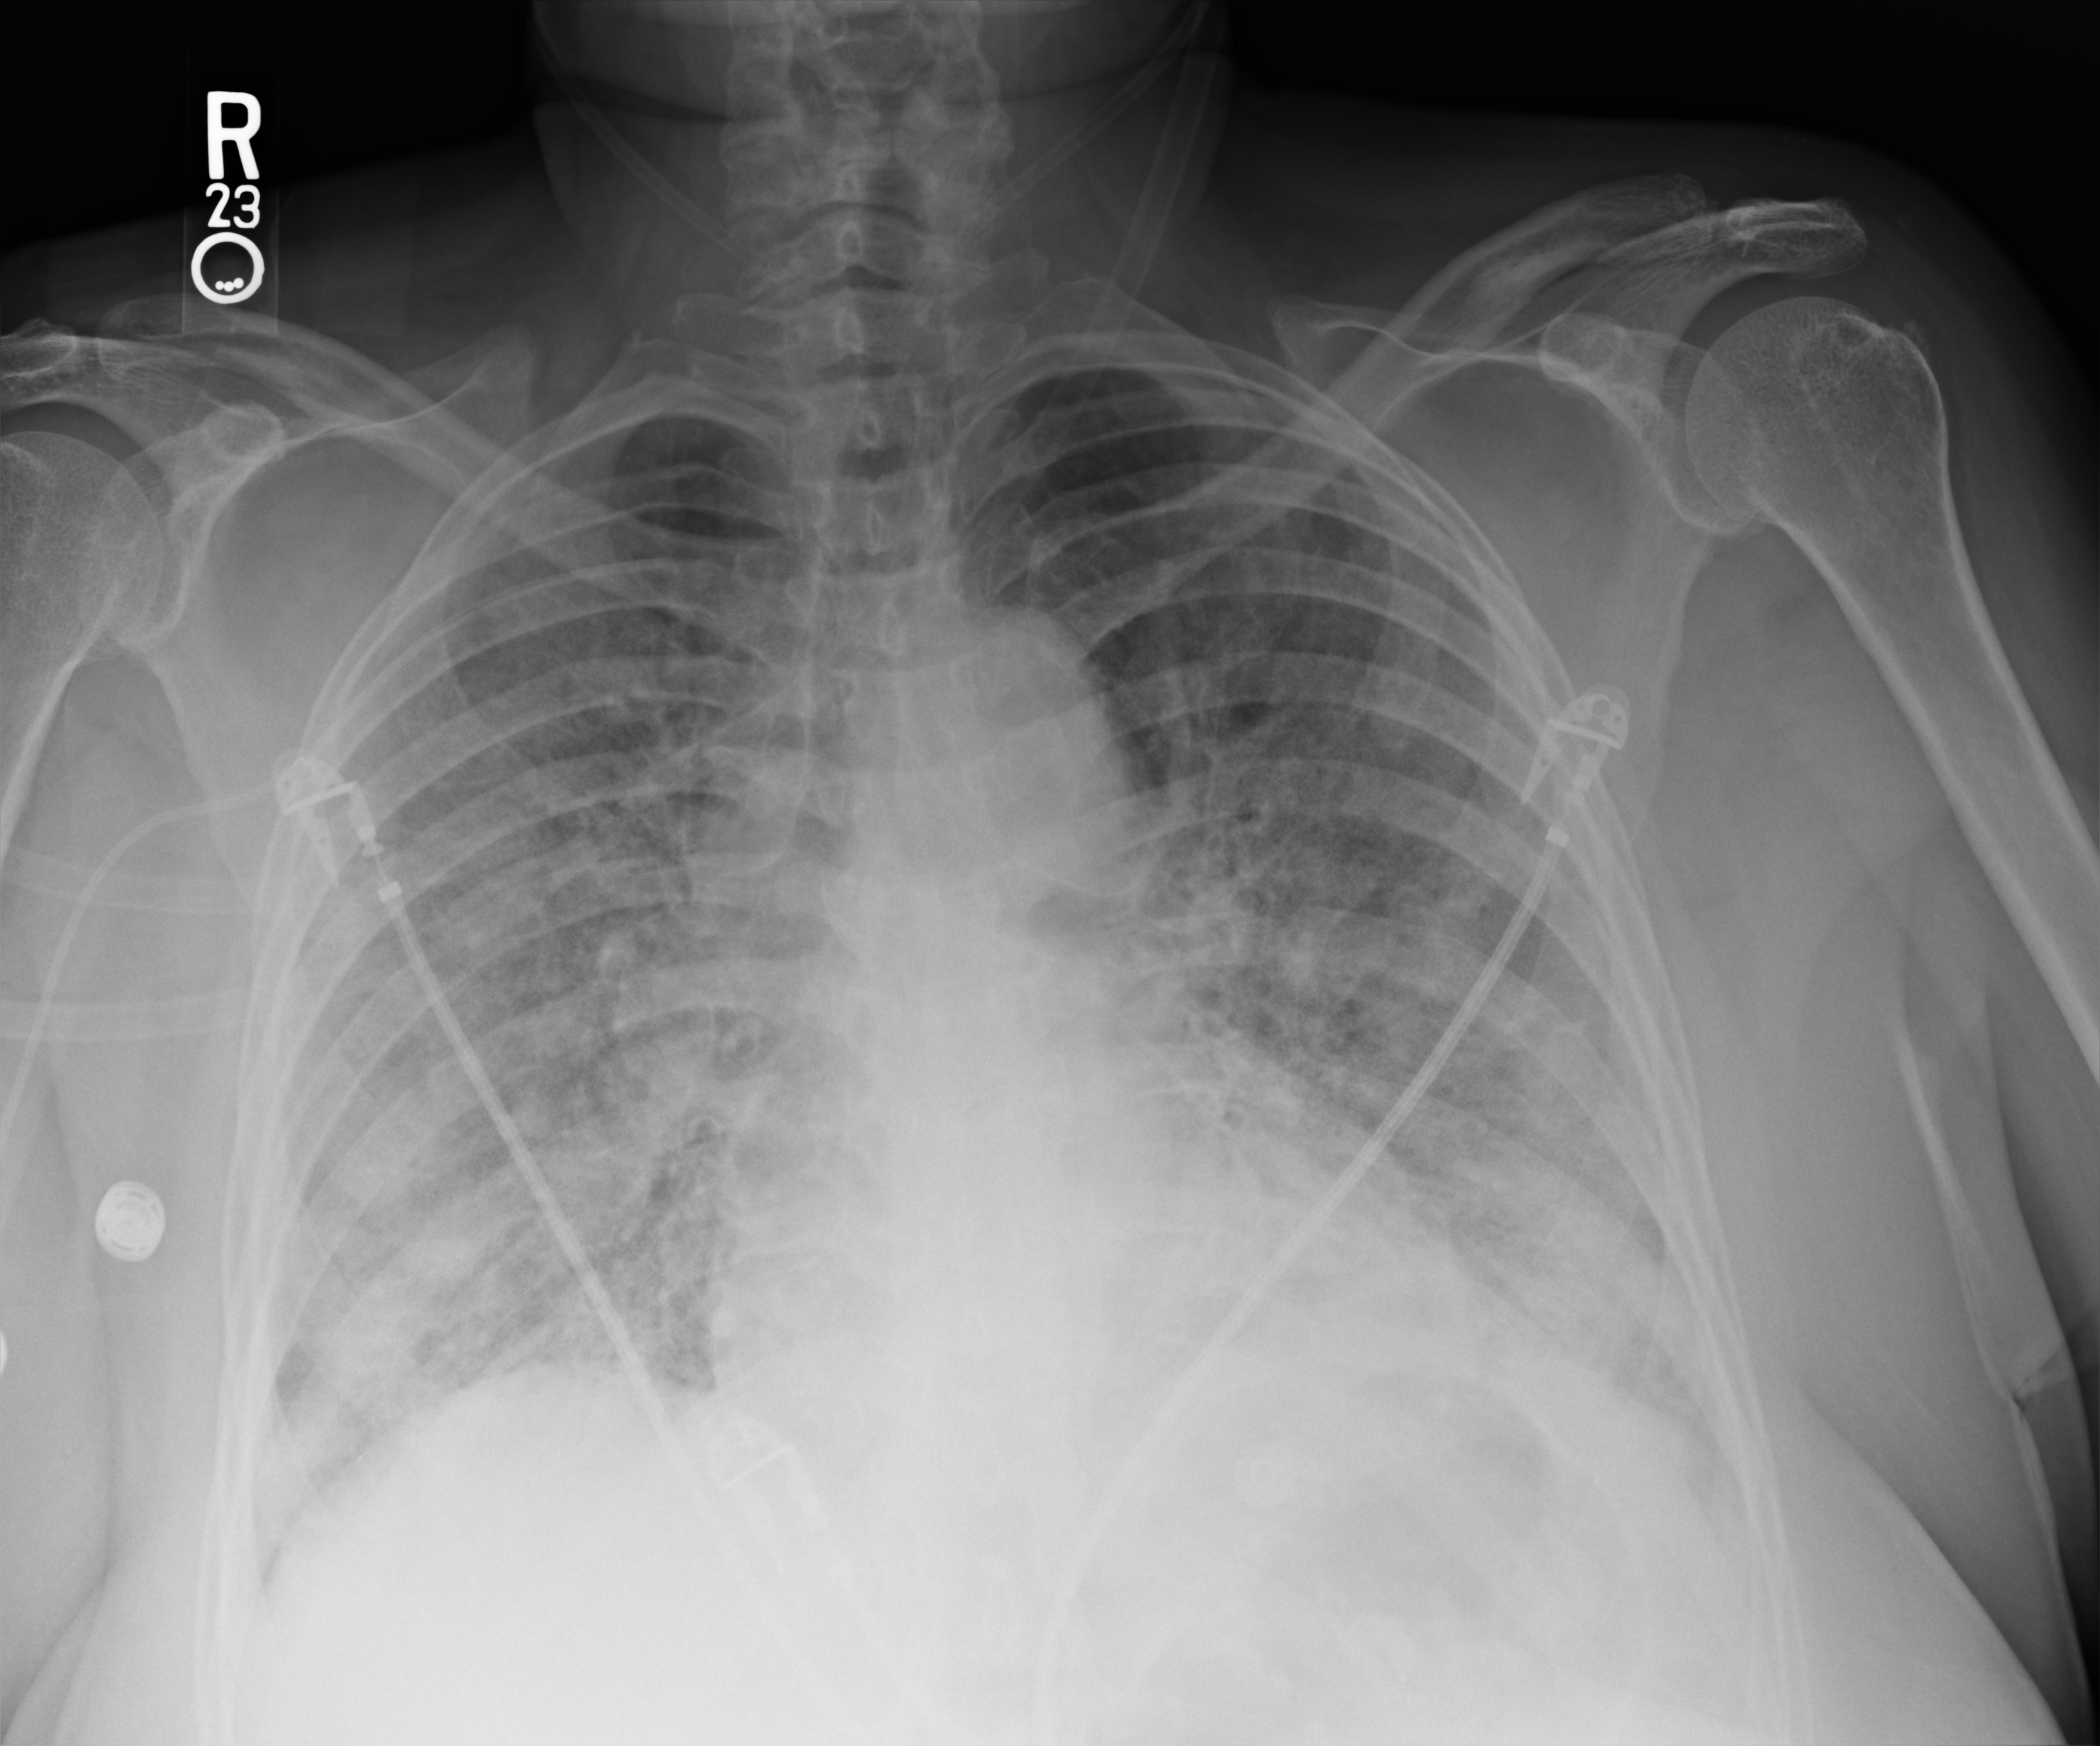
Chest X-ray (portable); anteroposterior (AP) projection. Female patient hospitalised with COVID-19, age 75–90 years.
Admission-level facts for this patient (not findings on this image; timing relative to this image not recorded): length of hospital stay: 26 days; mechanically ventilated during this hospital stay: yes; smoking status (admission record): never.